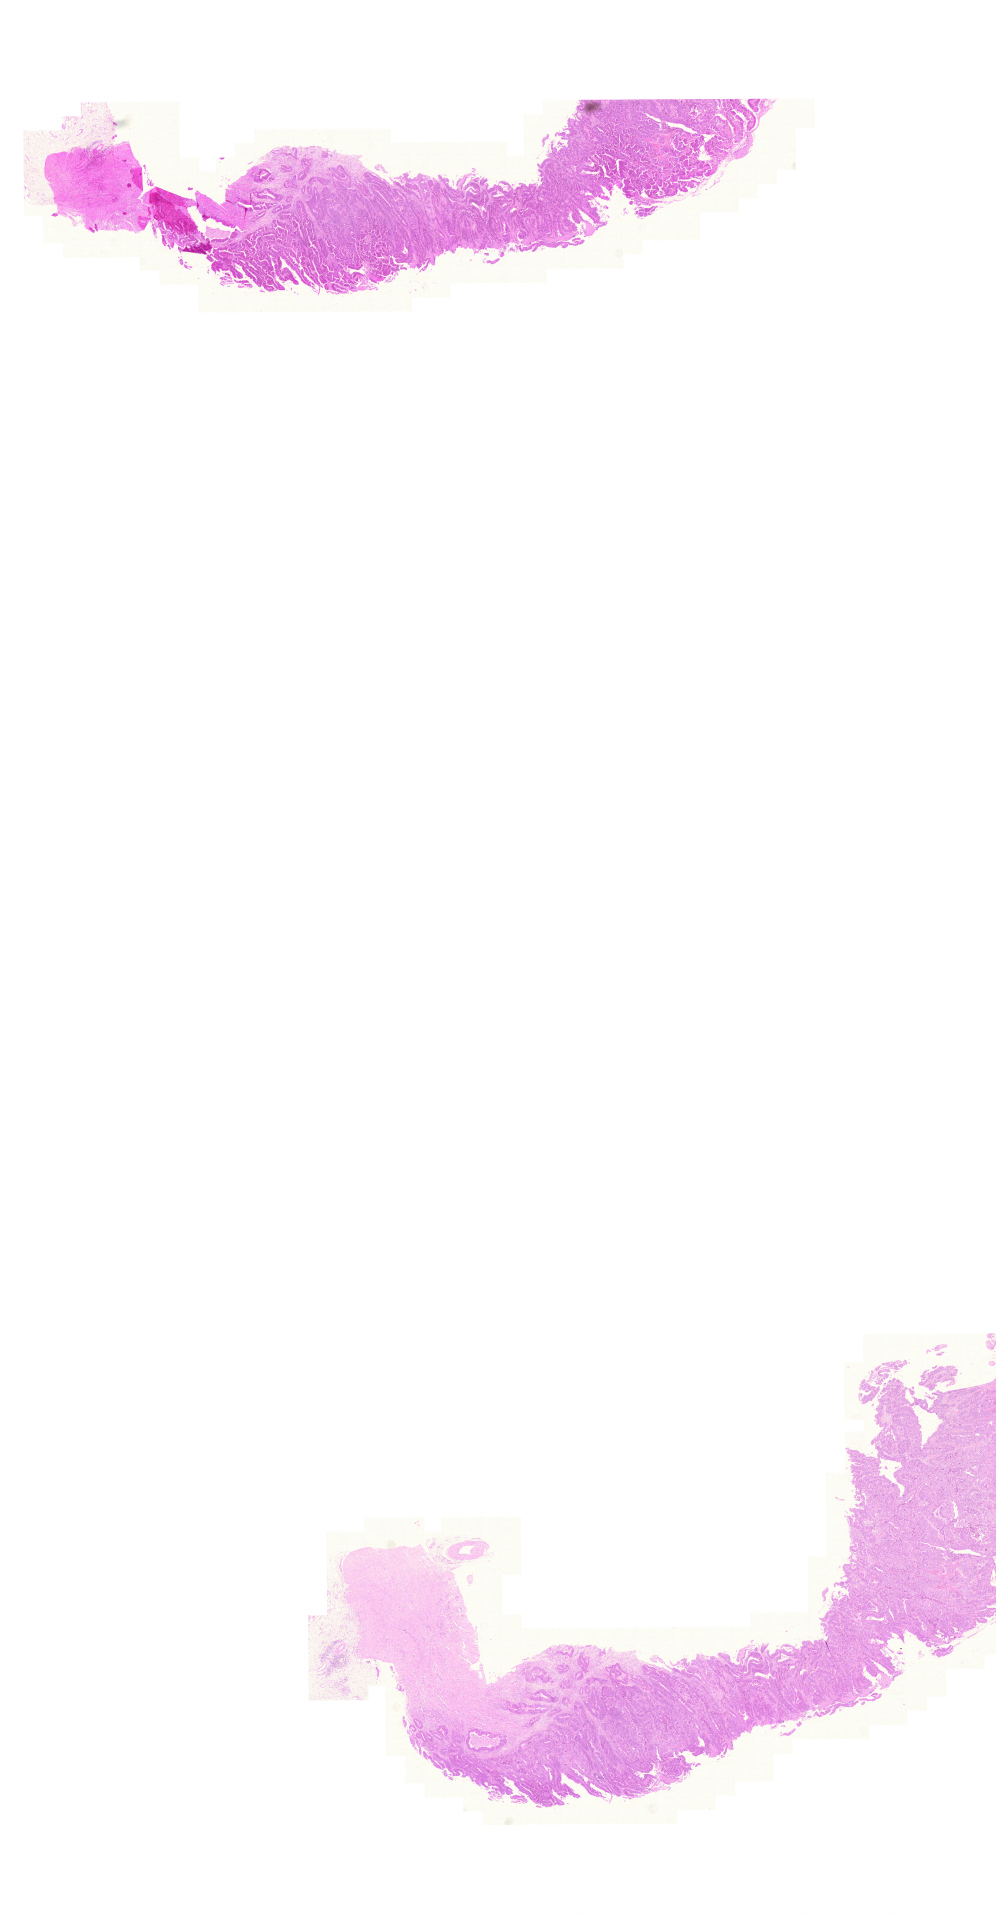
Digitized H&E tissue section (whole slide) — whole scanned area (about 14.8 x 28.5 mm) shown as a low-resolution overview, formalin-fixed paraffin-embedded (FFPE) diagnostic section, sample: primary tumour, rectum. Male, age 66 years at initial diagnosis.
Diagnosis: Adenocarcinoma, NOS.